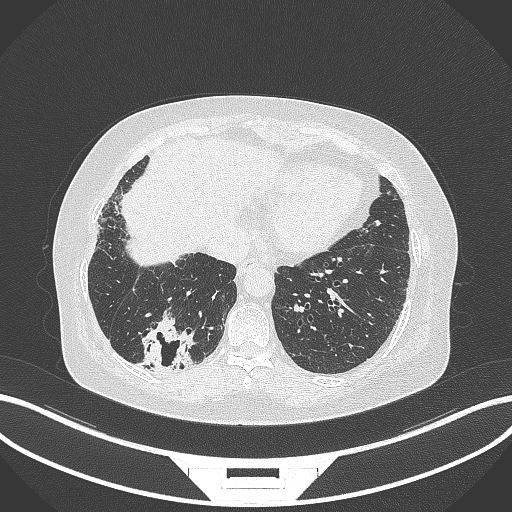
Chest CT, one axial slice. Slice 52 of 296 in the series (ordered by position). Lung window (W 1500 / L -600 HU). 512 × 512 image matrix, field of view 400 × 400 mm. Female patient, age 65 years. Case-level facts recorded for this patient, not image findings: clinical TNM (as recorded): T2b N1 M0; histopathological grade: G1.
Annotated regions visible in this slice (rectangle marked by the reading radiologist):
- lung tumour (recorded histology: adenocarcinoma): box from (x=137, y=311) to (x=199, y=374) px